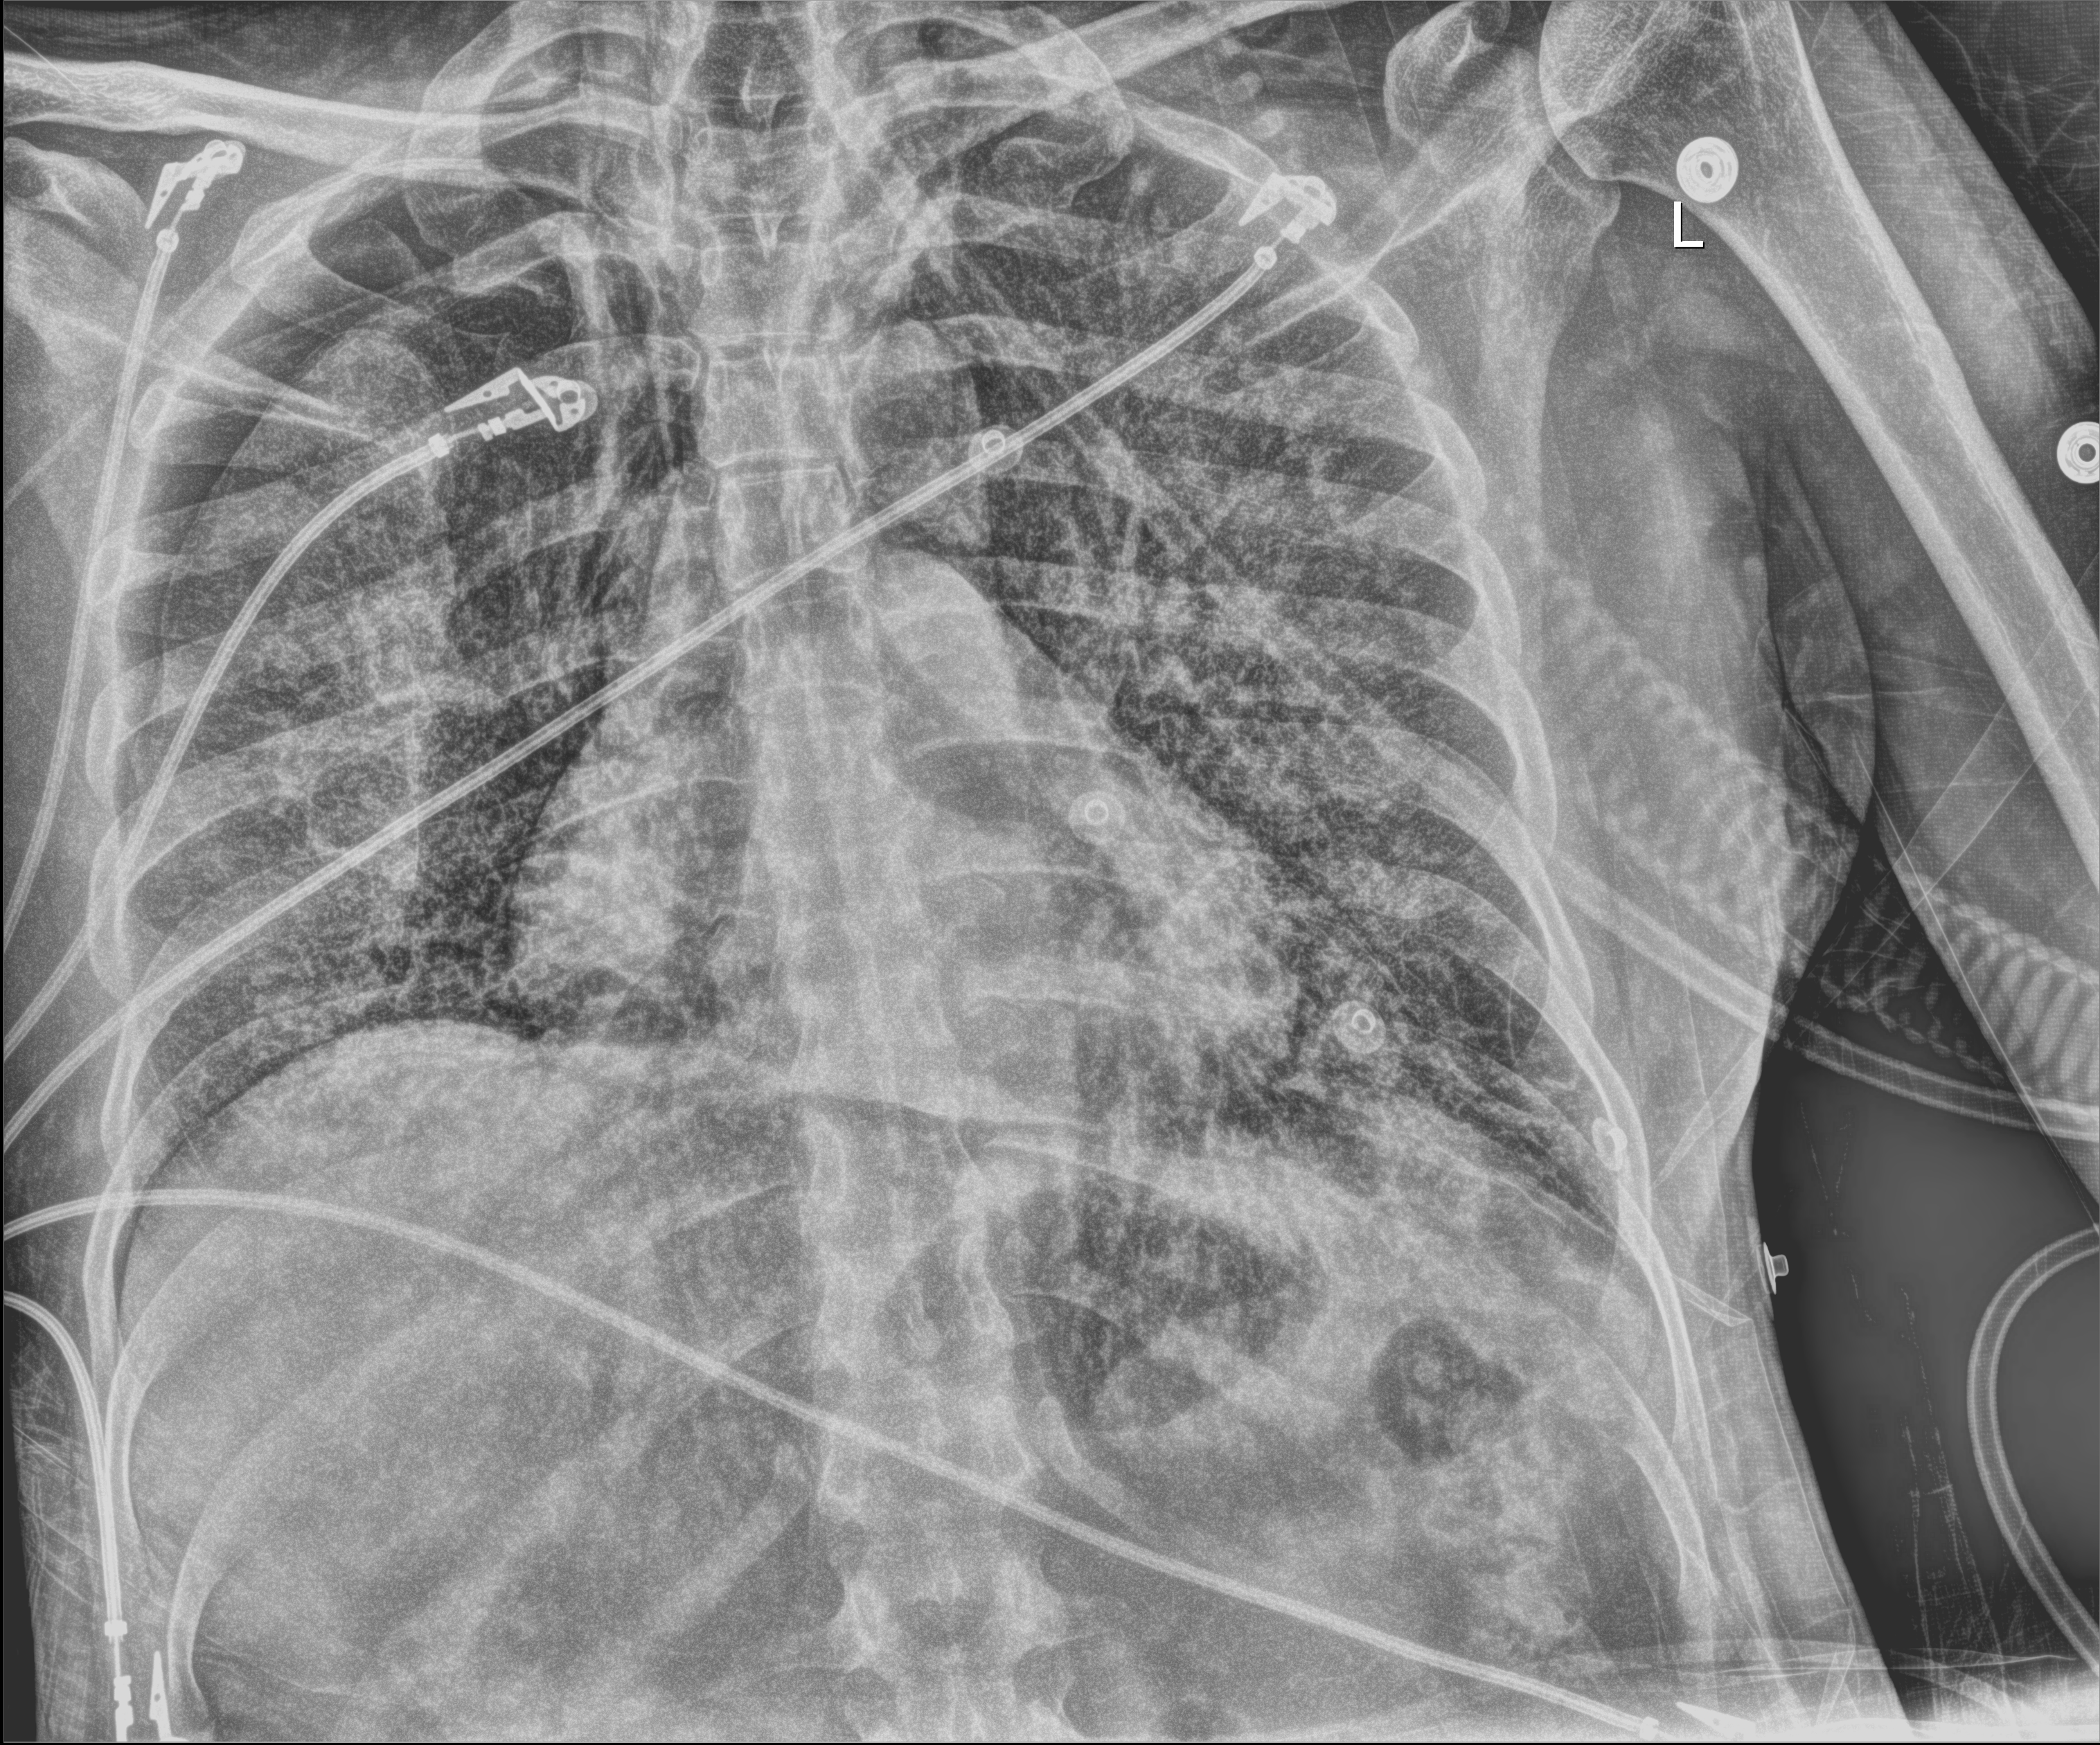
Bedside chest radiograph (digital radiography), anteroposterior (AP) projection. Adult patient hospitalised with COVID-19, age 18–59 years.
Admission-level facts for this patient (not findings on this image; timing relative to this image not recorded):
- admitted to intensive care during this hospital stay: yes
- length of hospital stay: 41 days